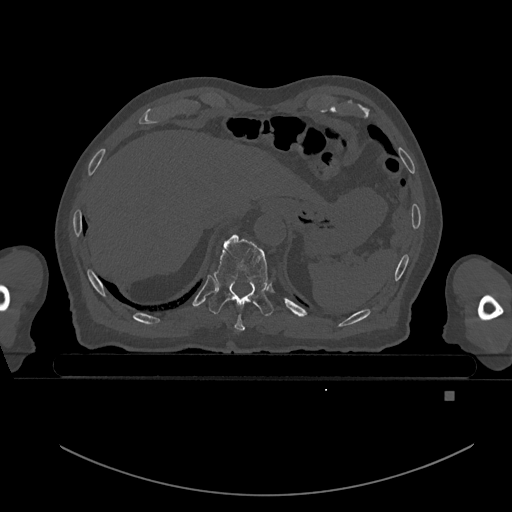
CT including the spine, one axial slice. Bone window (W 1800 / L 400 HU). 0.5 mm slice thickness. 512 × 512 image matrix, field of view 456 × 456 mm. Patient: male, 82 years. From the clinical record (not read from this slice): primary cancer: prostate; vertebrae with lytic lesions (as recorded): T11, T9, T8, T2.
Outlined on this slice (semi-automatic segmentation, software-assisted and operator-edited):
- T10 vertebra: bounding box <209,234,274,317> (left, top, right, bottom; pixels)
- T9 vertebra: <234,314,245,332>